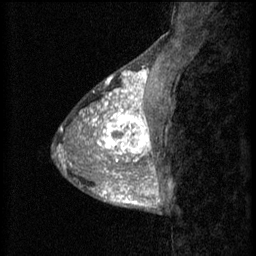
Breast MRI (dynamic contrast-enhanced), one sagittal slice; slice 19 of 60 in the series (ordered by position); 3 images stored at this slice position (order not interpretable as contrast timing); 1.5 T; TE 4.2 ms, TR 8.2 ms; 2 mm slice thickness; 256 × 256 image matrix, field of view 180 × 180 mm. Female patient, age 38 years.
Outlined on this slice (semi-automatically segmented with operator editing):
- analysis volume of interest (the breast-tissue region the enhancement analysis was run in; not a lesion): bounding box <95,106,157,171> (left, top, right, bottom; pixels)
- tumour enhancement mask (voxels above the 70 % enhancement threshold inside the analysis volume of interest): <95,106,155,171>